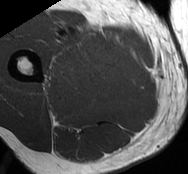
MRI of an extremity soft-tissue mass, one axial slice; slice 25 of 93 in the series (ordered by position); MR volume resampled by the dataset authors to the PET/CT grid (not the native acquisition matrix); 3.27 mm slice thickness; 188 × 174 image matrix, field of view 184 × 170 mm. Male patient. Case-level facts recorded for this patient, not image findings: histological type: undifferentiated - pleiomorphic; grade: high; site of the primary tumour: right thigh.
Annotated regions visible in this slice (expert contour drawn on MRI and transferred to this co-registered scan by the dataset authors):
- gross tumour volume including surrounding oedema: box from (x=47, y=26) to (x=128, y=84) px
- gross tumour volume (mass): (x=100, y=51)–(x=123, y=68)